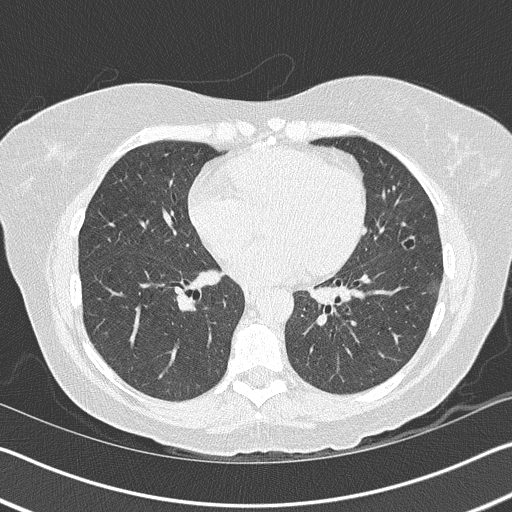
Axial slice from a low-dose chest CT screening exam. Baseline screening round. Lung window (W 1500 / L -600 HU). 2 mm slice thickness. Lung (sharp) reconstruction kernel (B50f). Slice 72 of 157 in the series. 512 × 512 image matrix, field of view 340 × 340 mm. Female, age 63 years at enrolment. Current smoker at enrolment.
Expert-annotated lung lesion, bounding box (x1, y1, x2, y2) in pixels: (386, 221, 438, 261). The screening reader recorded 3 non-calcified nodules or masses ≥4 mm on this exam (right upper lobe, left upper lobe, lingula); which of them this box marks is not recorded. Lung cancer was diagnosed 1029 days after this screen (after the third annual screen): bronchiolo-alveolar adenocarcinoma, NOS, lingula, stage IA (AJCC 6th edition), 14 mm at pathology.